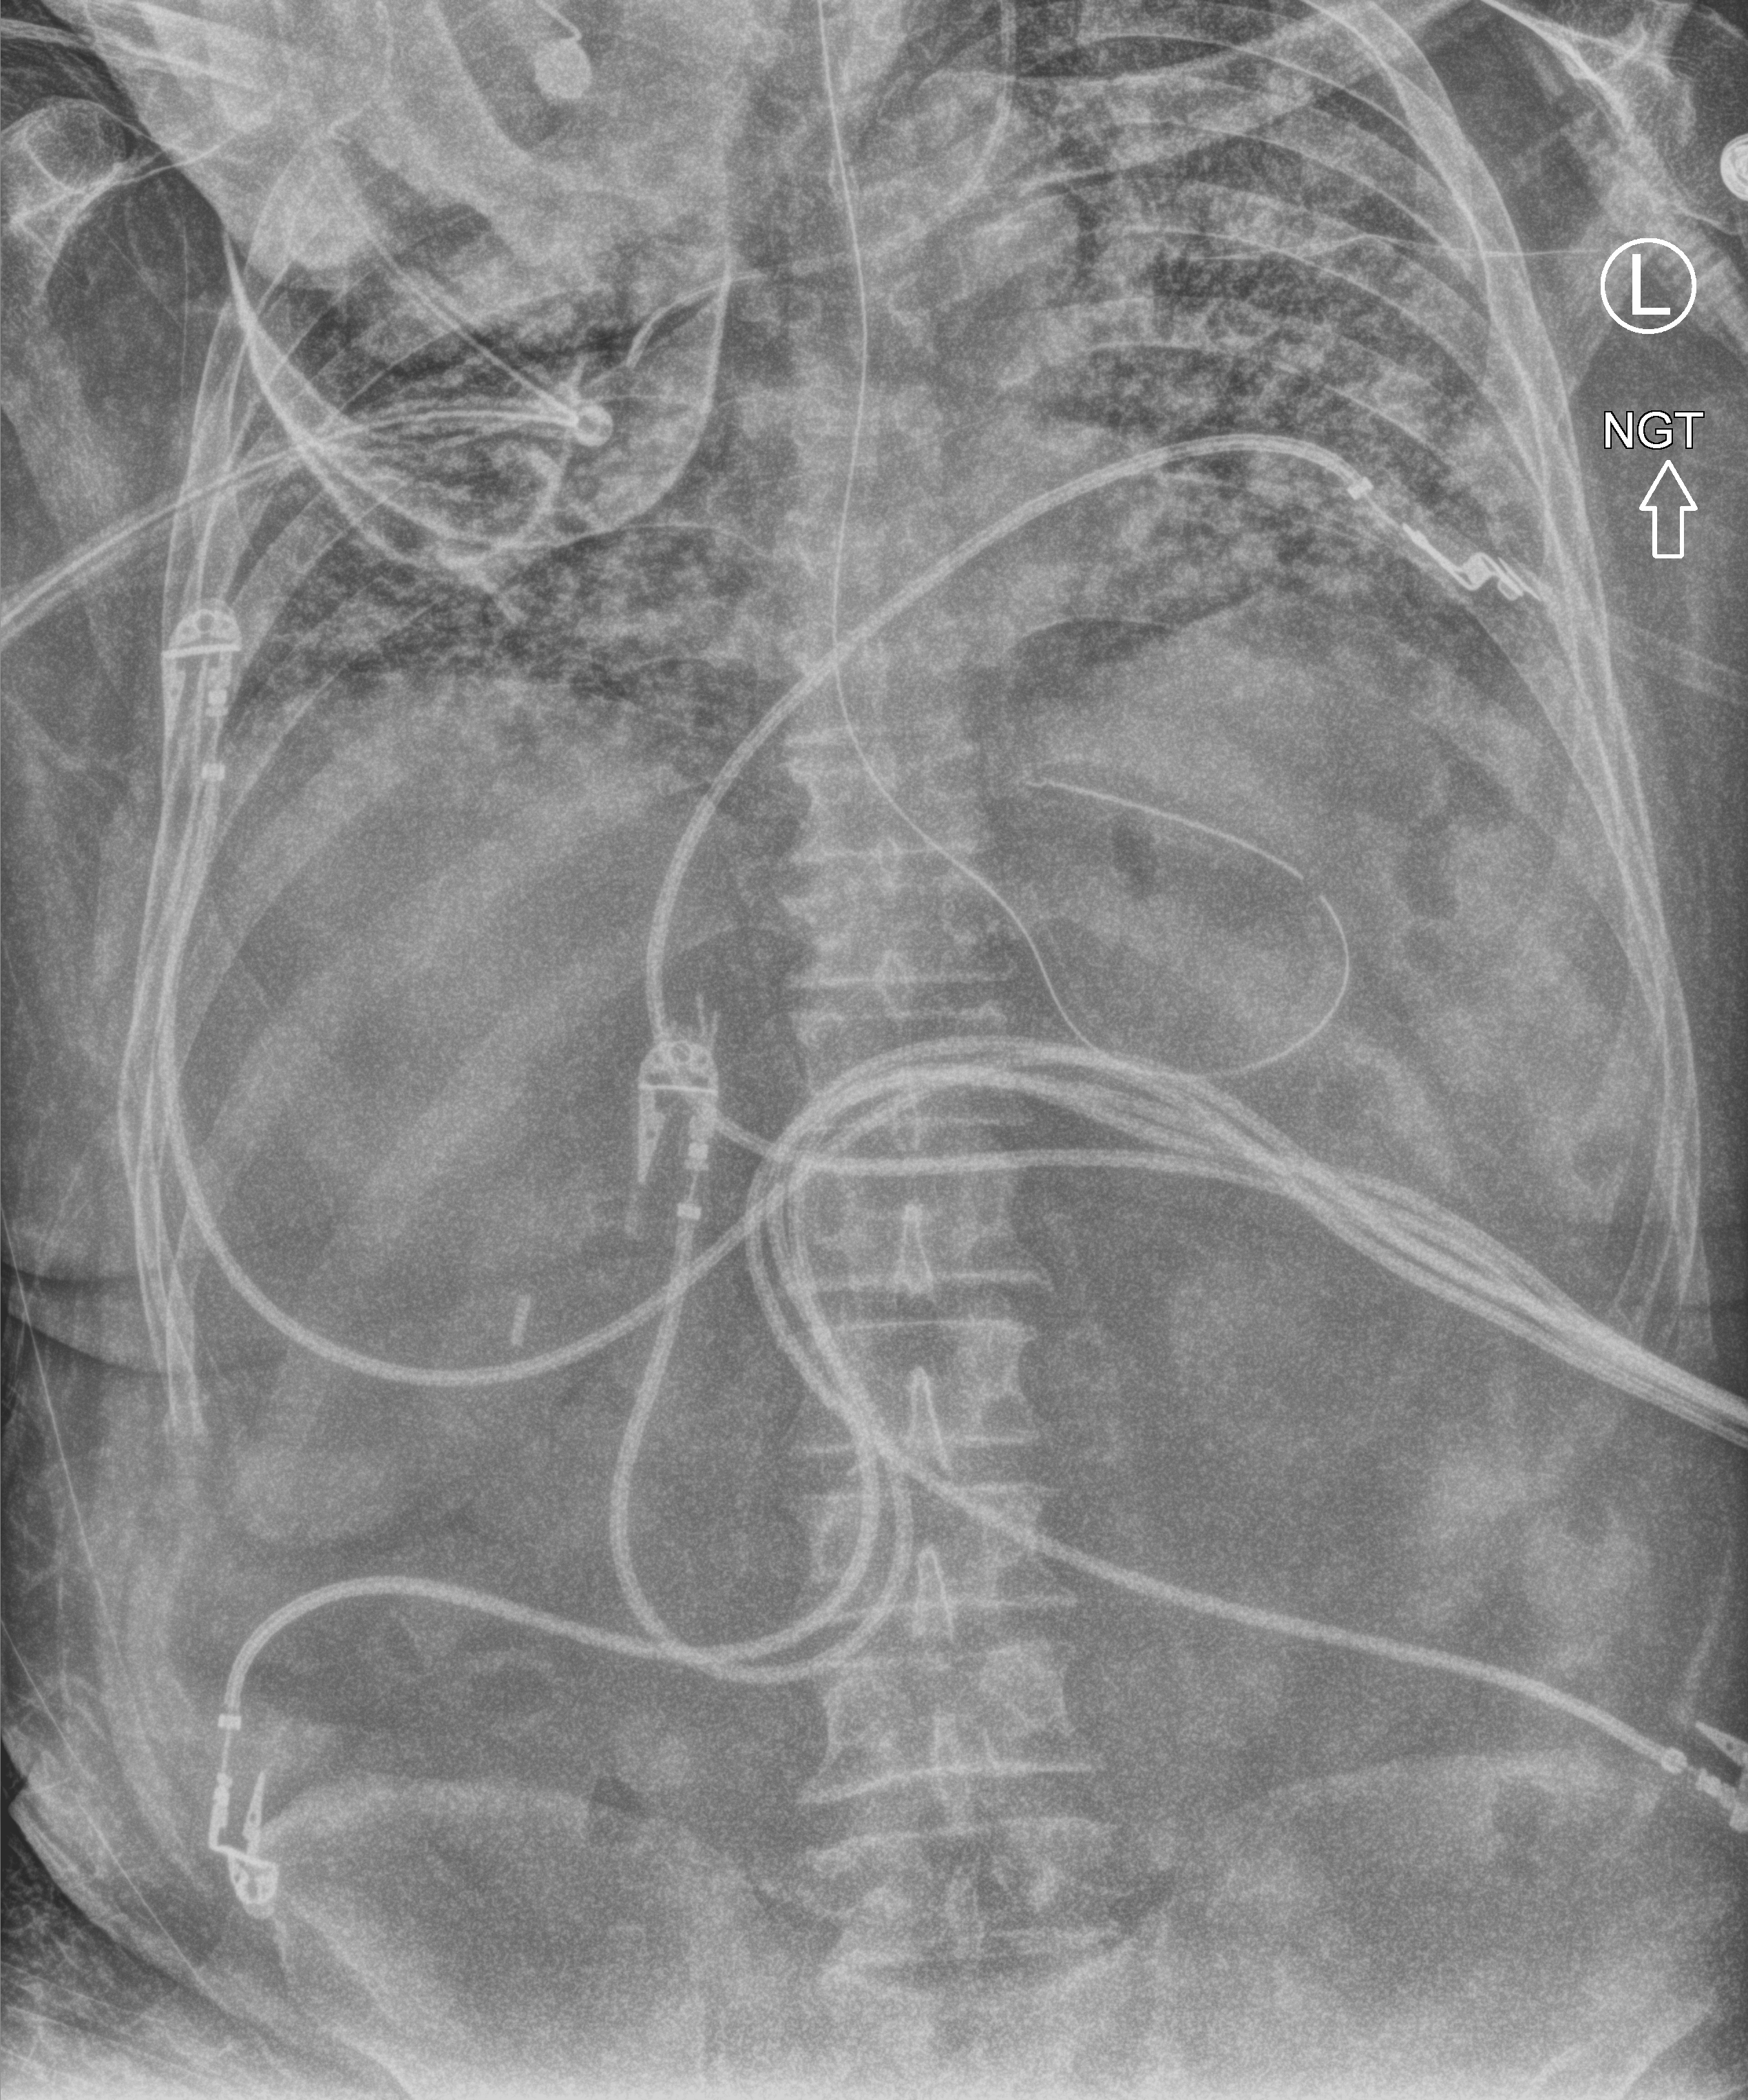
Chest X-ray (portable), anteroposterior (AP) projection. Patient hospitalised with COVID-19; male, aged 60–74 years.
Admission-level facts for this patient (not findings on this image; timing relative to this image not recorded):
- smoking status (admission record): never
- length of hospital stay: 23 days